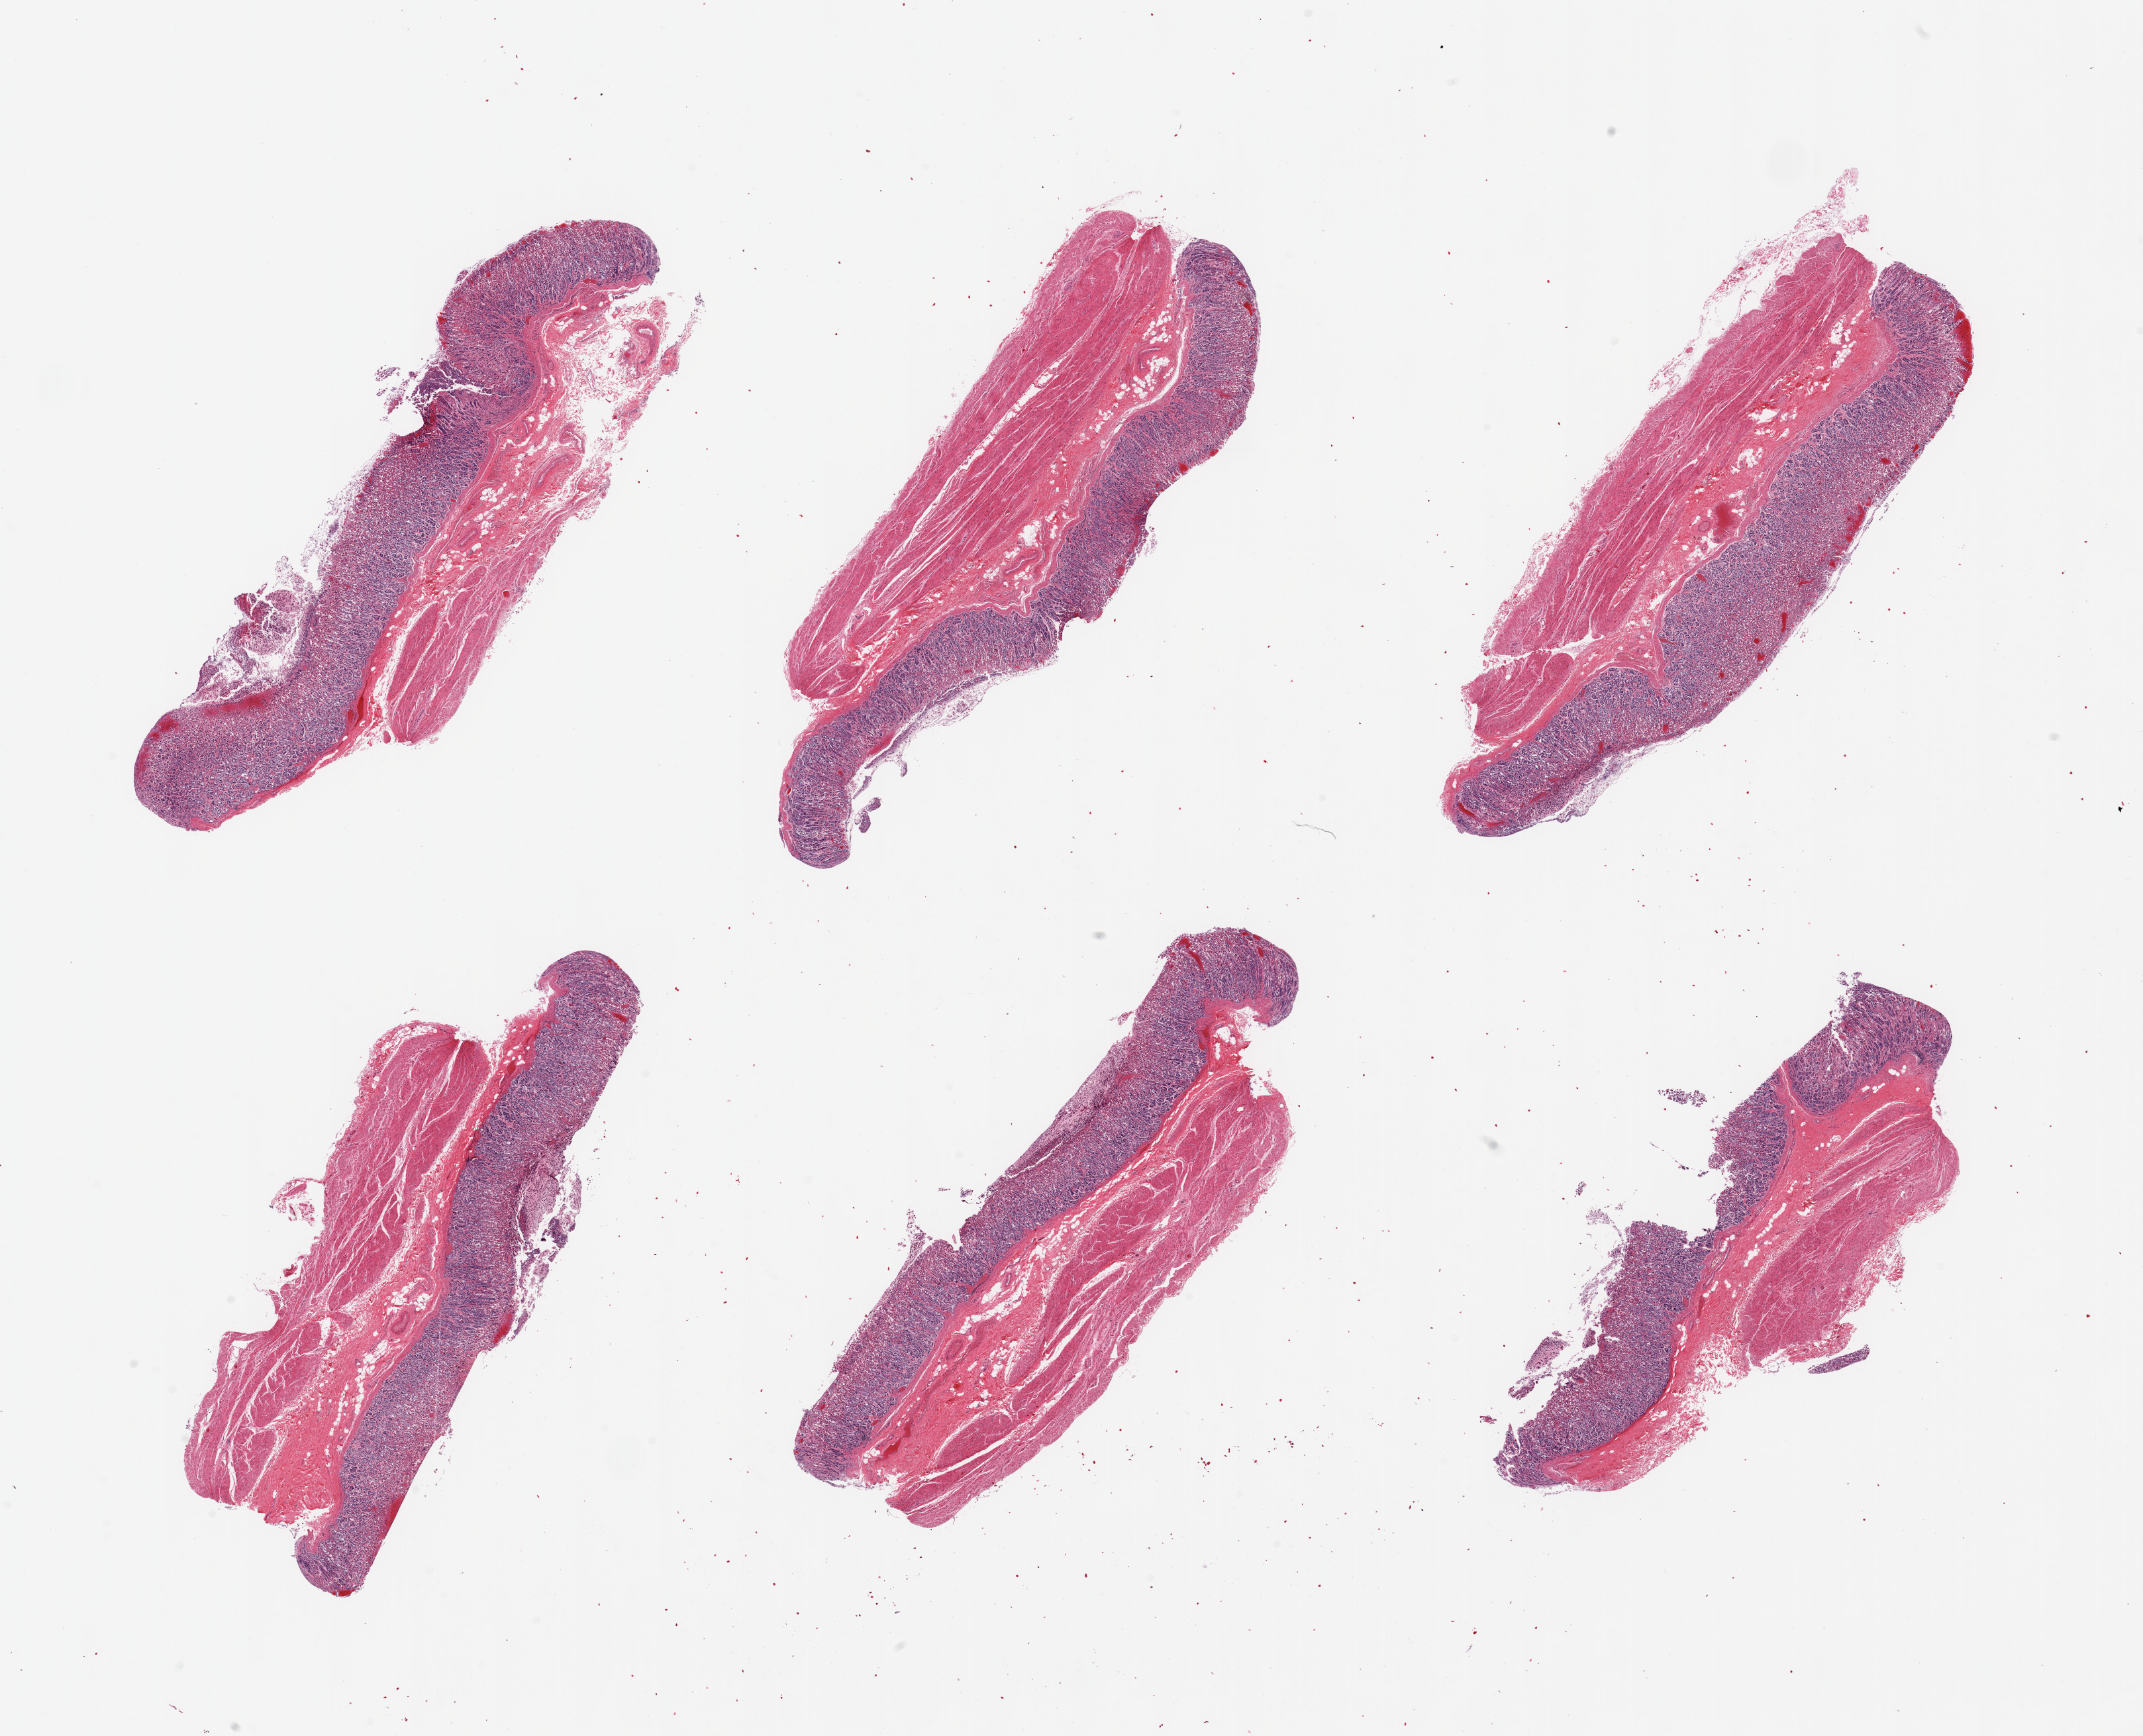
Whole-slide image, haematoxylin and eosin stain, brightfield — shown as a low-resolution overview of the whole scanned area (about 25.6 x 20.7 mm, slide scanned at 20x); PAXgene-fixed, paraffin-embedded tissue; sampled site (target tissue): stomach; tissue donor sample. Donor sex: male.
Reviewer comment on this tissue sample: 6 pieces, target mucosa up to ~1mm, ~30-40% thickness; deeper (basal)mucosa better preserved (score 1).